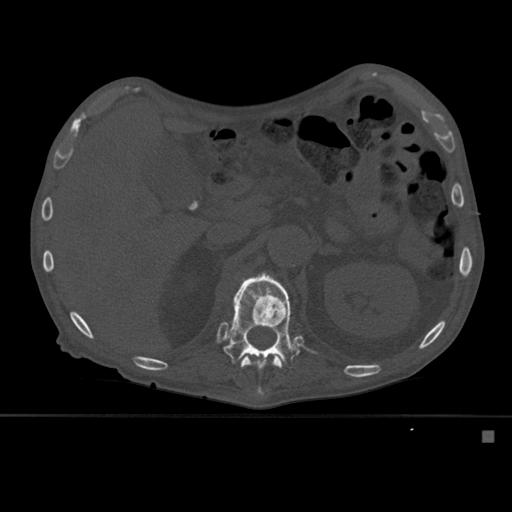
CT including the spine, one axial slice; position 261 of 527 along the scan axis; bone window (W 1800 / L 400 HU); 1.5 mm slice thickness; 512 × 512 image matrix. Male patient, age 78 years. Case-level facts recorded for this patient, not image findings: primary cancer: prostate.
Structures marked on this image (semi-automatic segmentation, software-assisted and operator-edited):
- L1 vertebra: bounding box (x1, y1, x2, y2) in pixels: (223, 272, 300, 396)
- T12 vertebra: (240, 356, 282, 369)